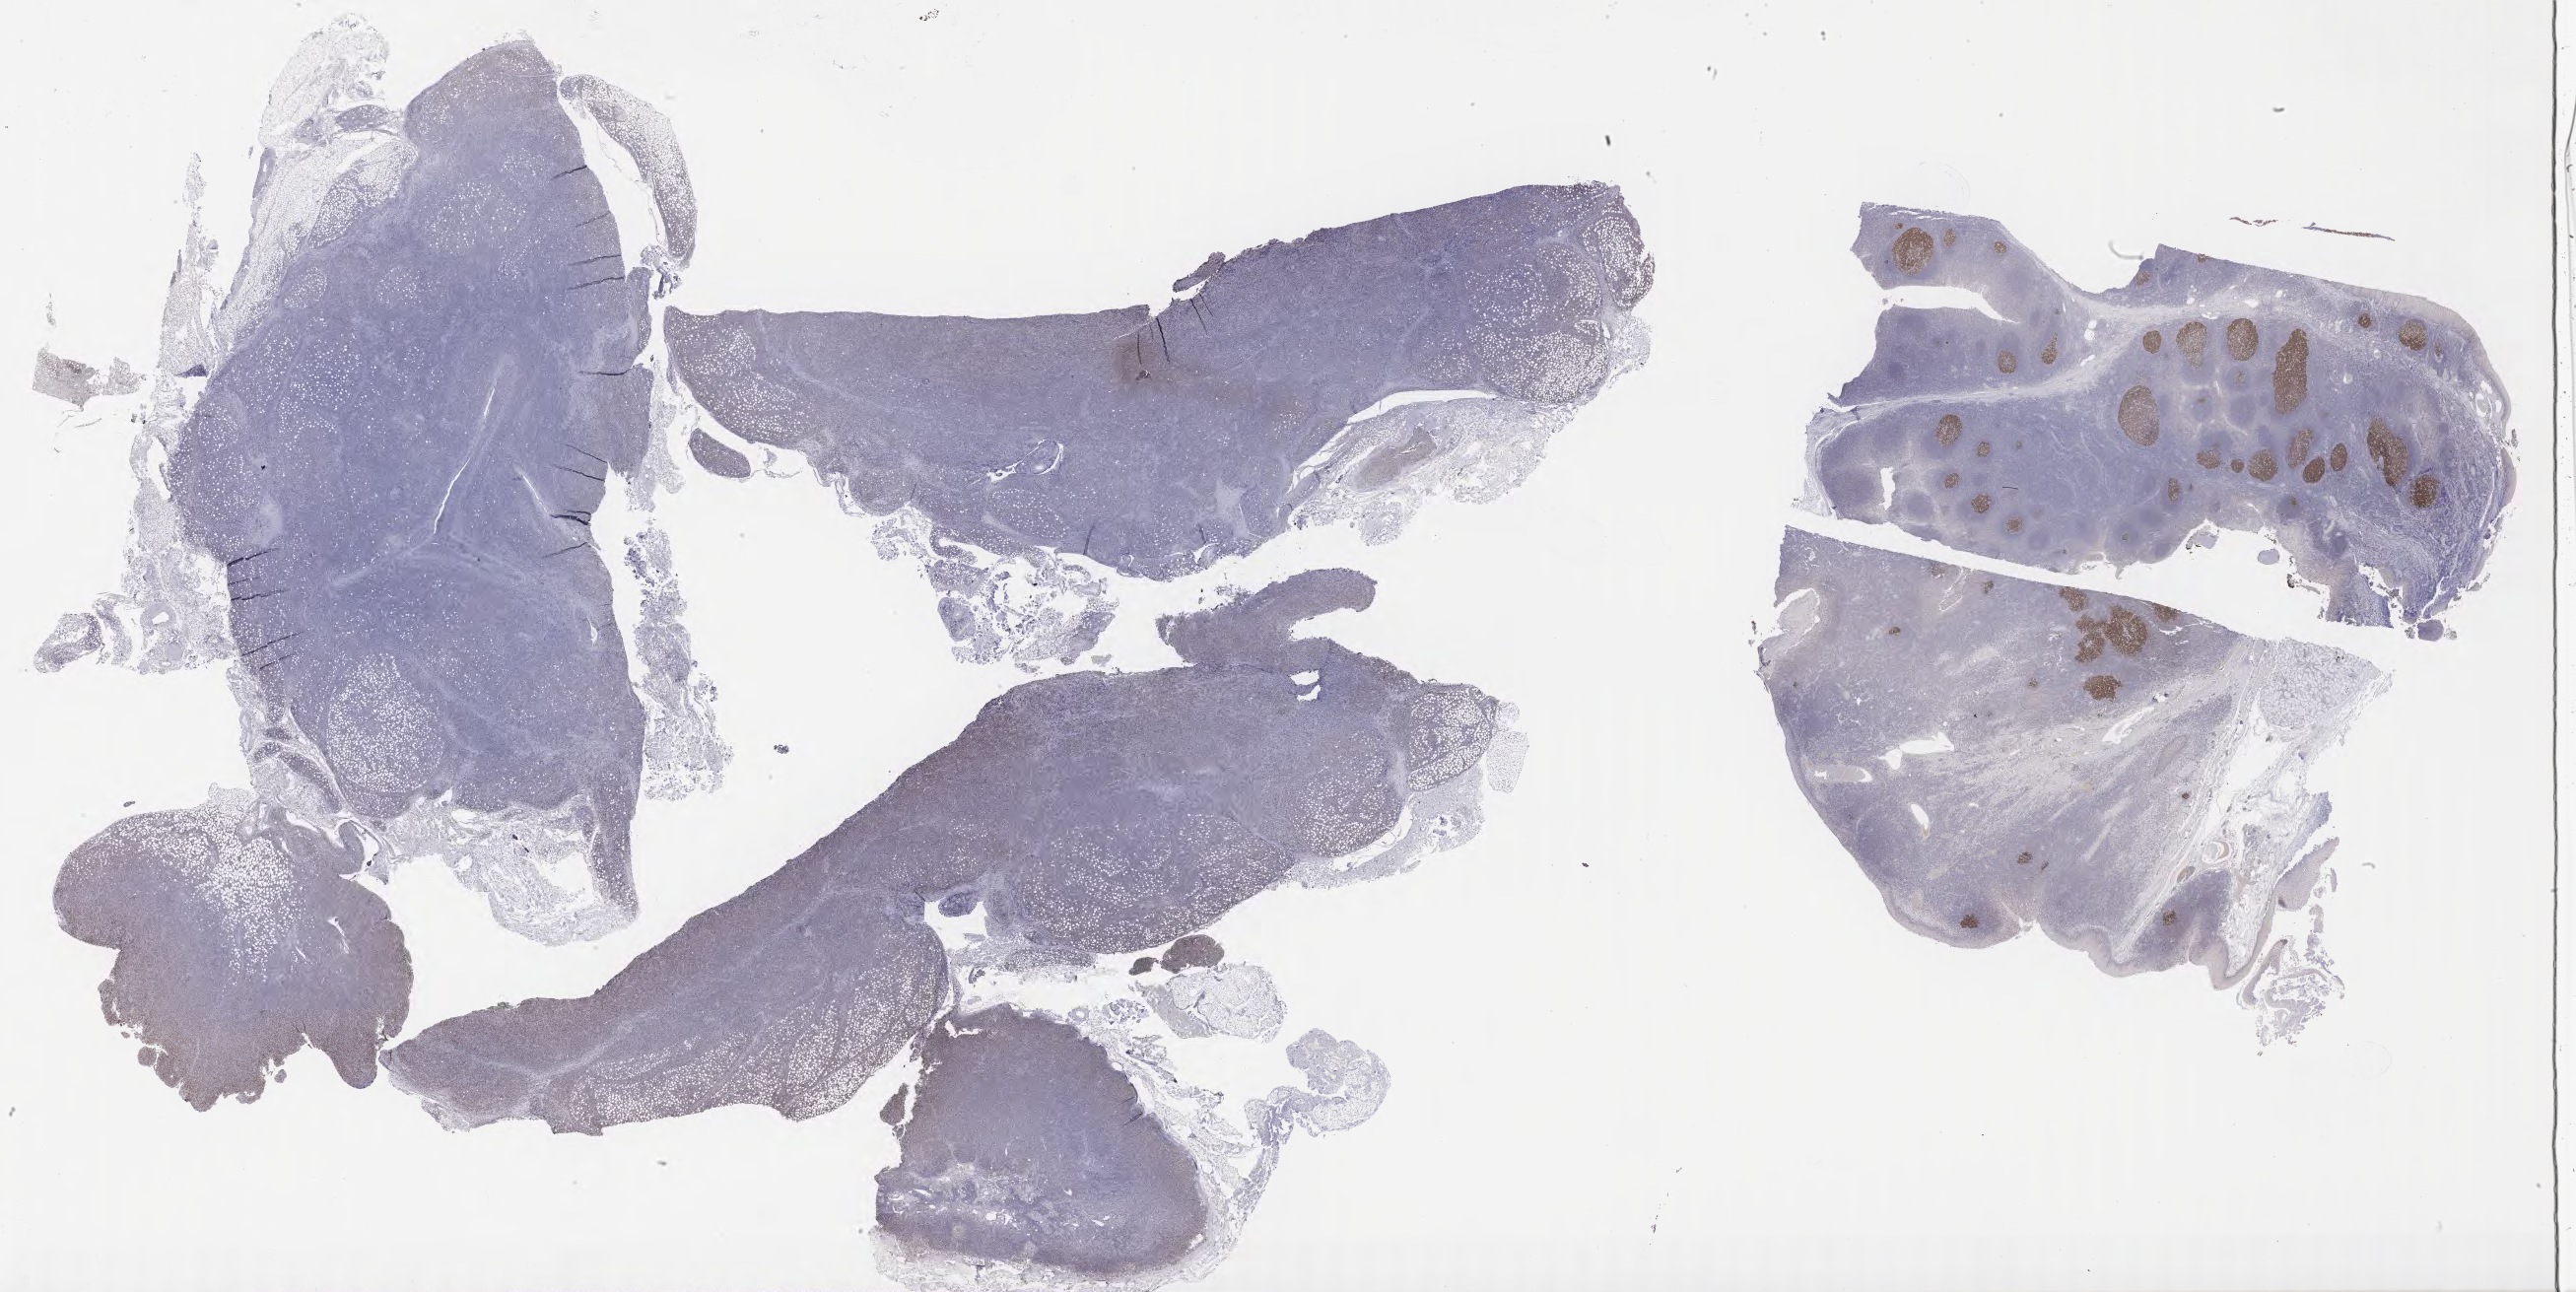
IHC for BCL6, whole-slide image — low-resolution overview of the scanned area, about 42.3 x 21.2 mm, tumor tissue, site: lymph node. Patient male; 68 years old.
Diagnosis: Diffuse large B-cell lymphoma, NOS.